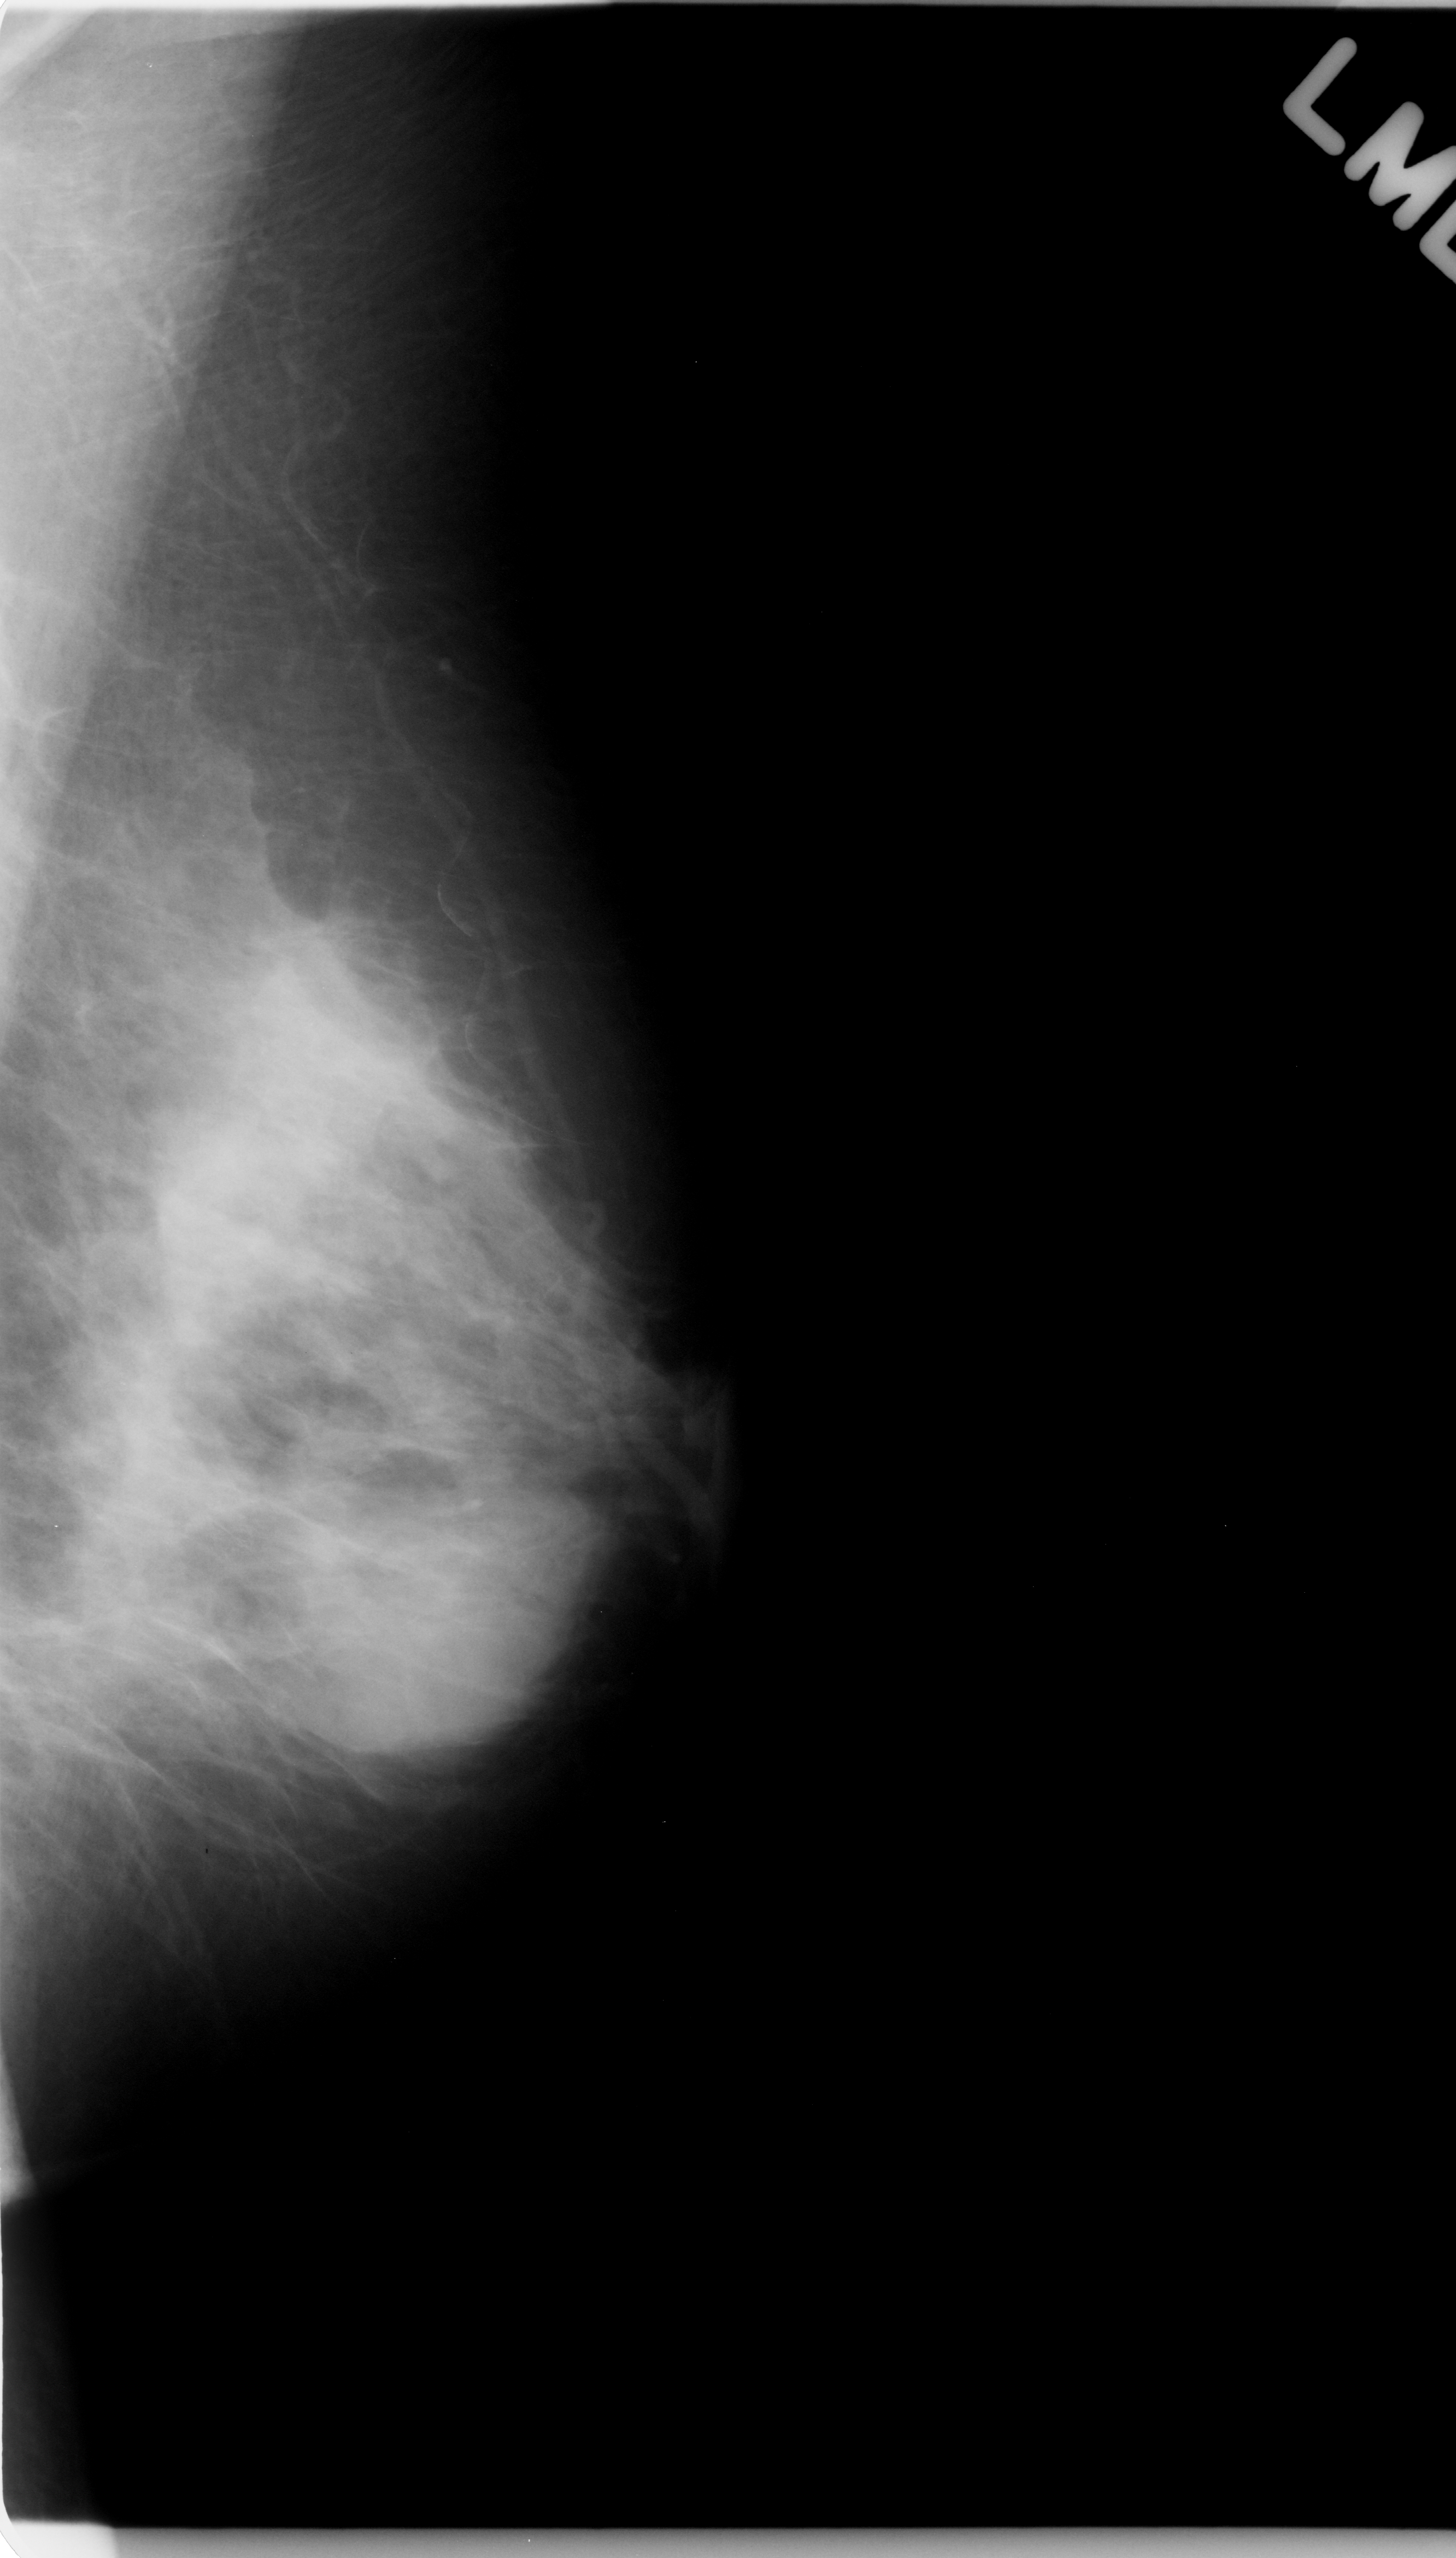
Mammogram (digitized film); left breast; mediolateral oblique (MLO) view; breast composition: heterogeneously dense (BI-RADS density category 3 of 4); 1456 × 2558 image matrix.
Marked abnormalities (boxes around the expert regions of interest):
- mass, shape oval, margins ill defined; BI-RADS assessment category 3; subtlety rating 4 on a 1 (subtle) to 5 (obvious) scale; pathology (as recorded): benign: bounding box <303,1463,599,1782> (left, top, right, bottom; pixels)